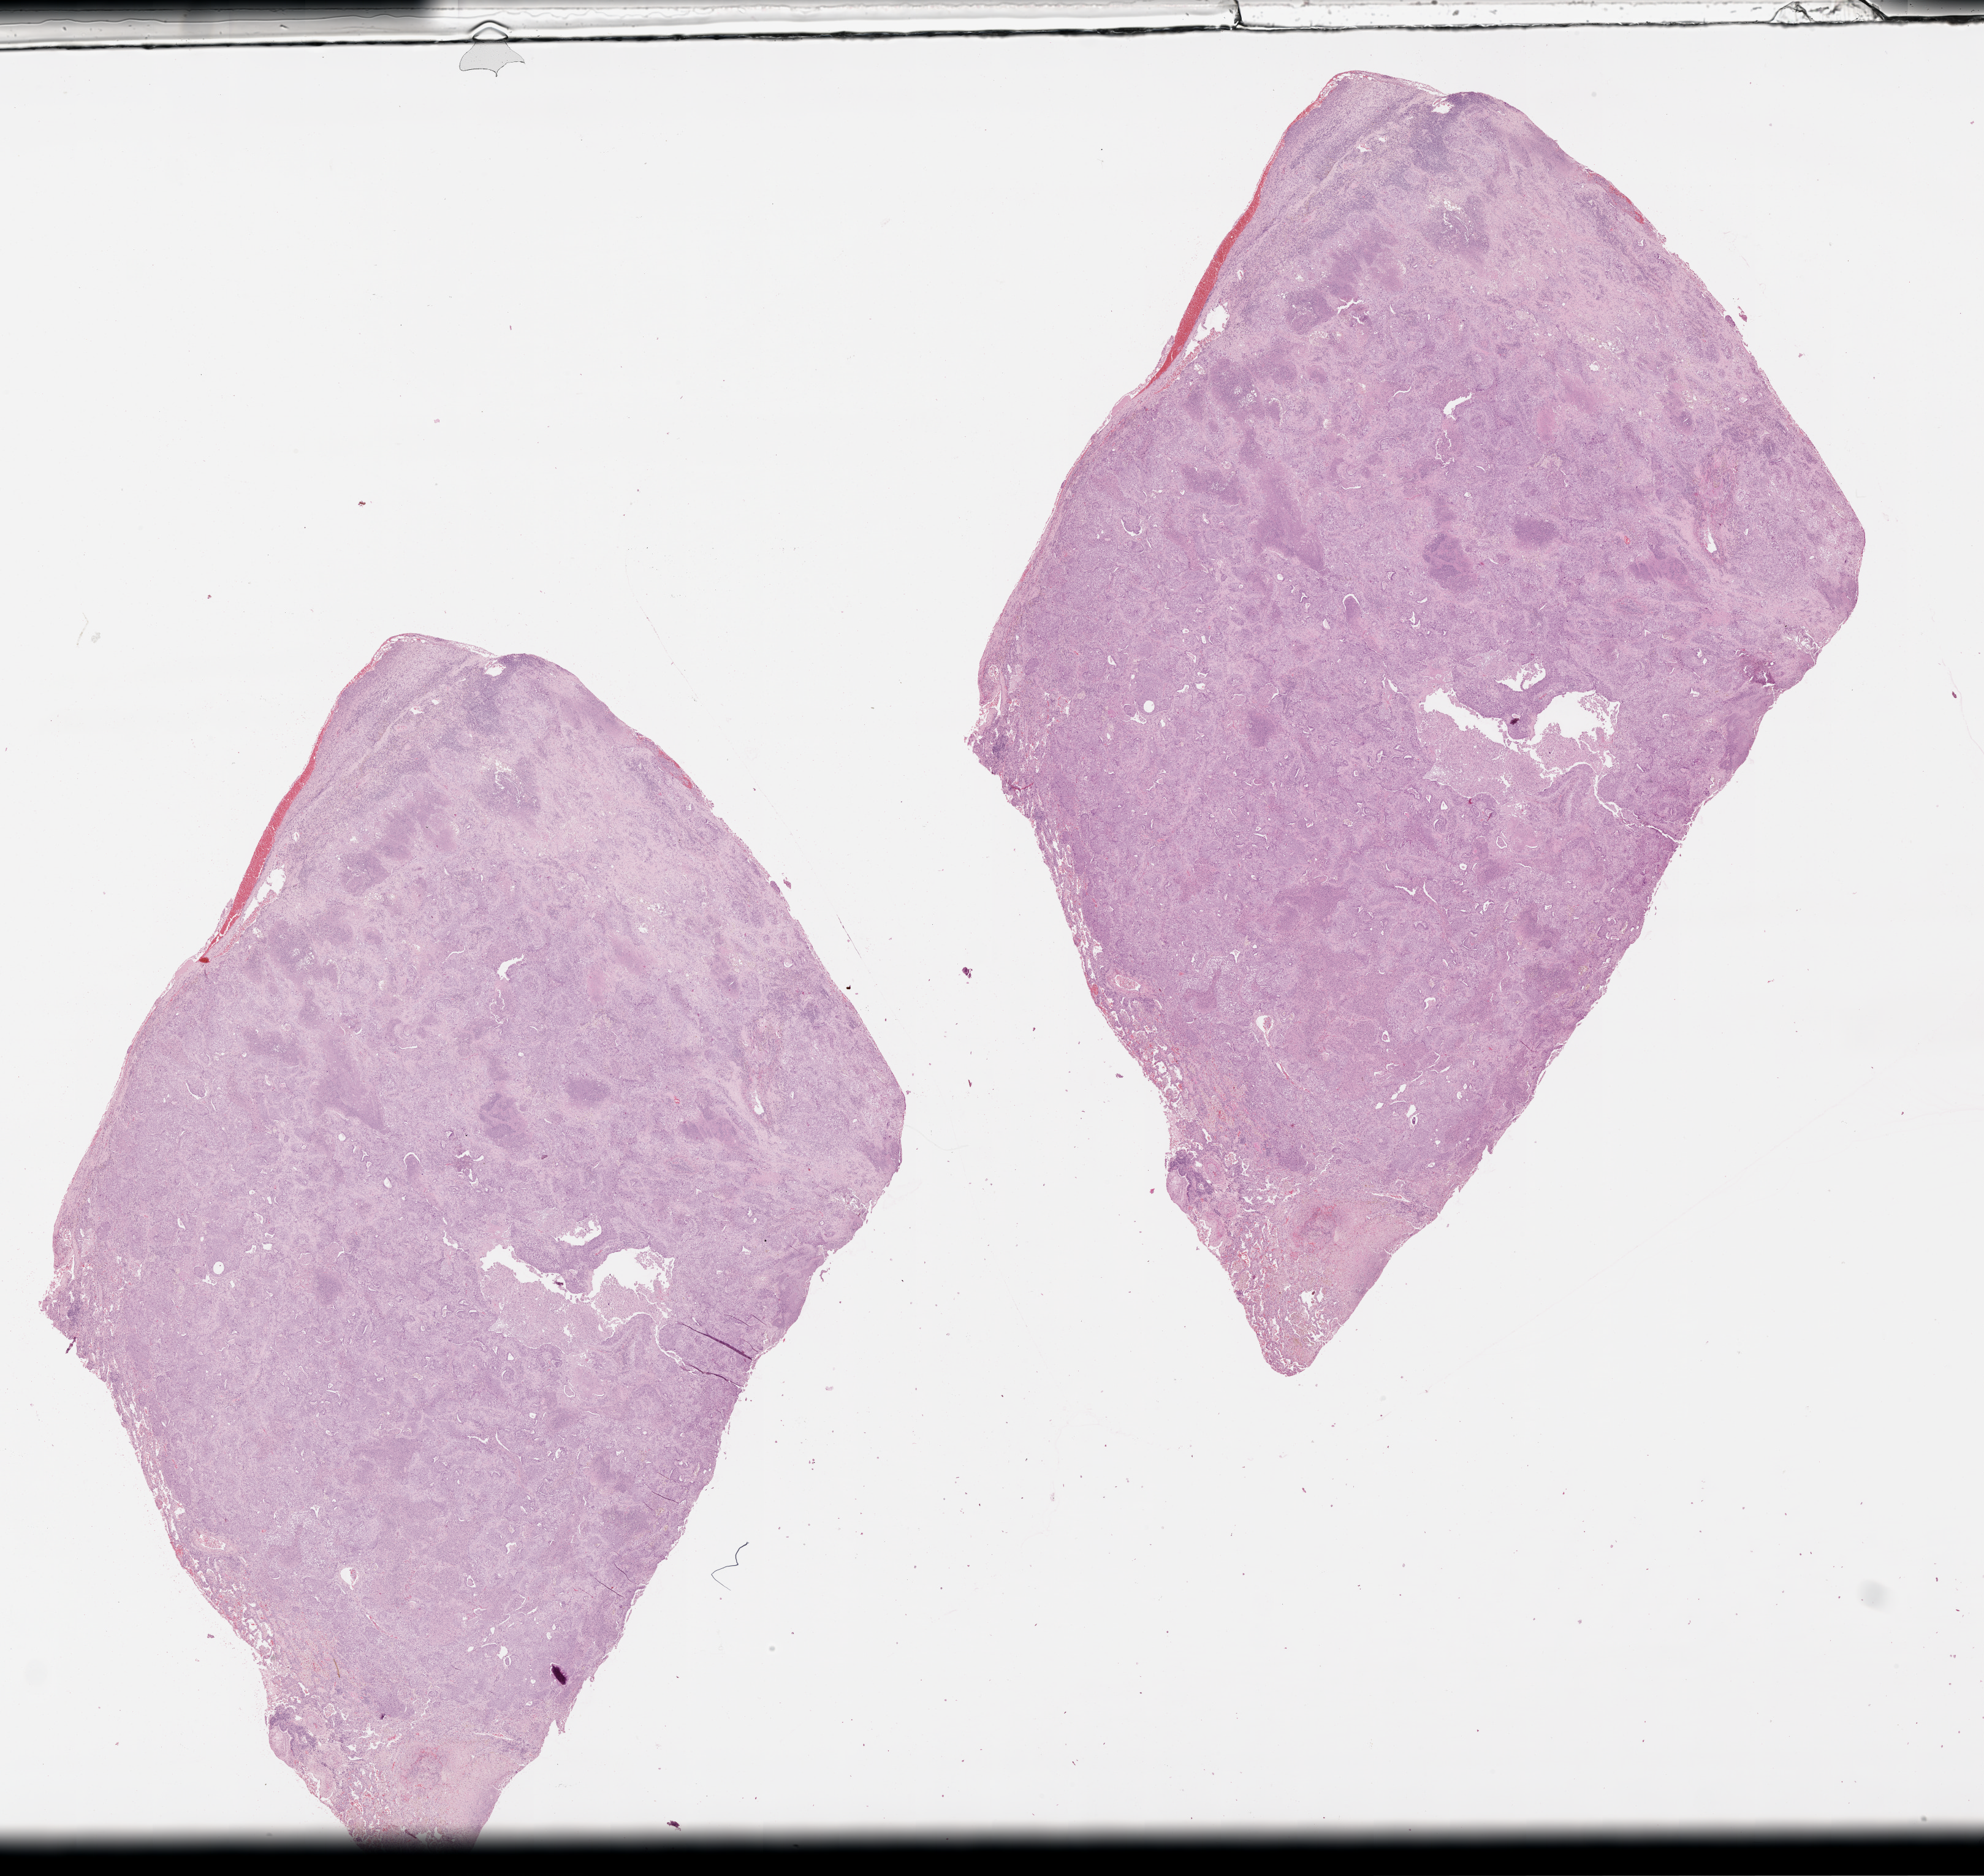
Whole-slide histology image, Hematoxylin and eosin (H&E) stained, shown as a low-resolution overview of the whole scanned area (about 26.1 x 24.6 mm); lung, tumour tissue. Patient: male, age 56 years.
Patient diagnosis (cohort enrolment): squamous cell carcinoma (lung).